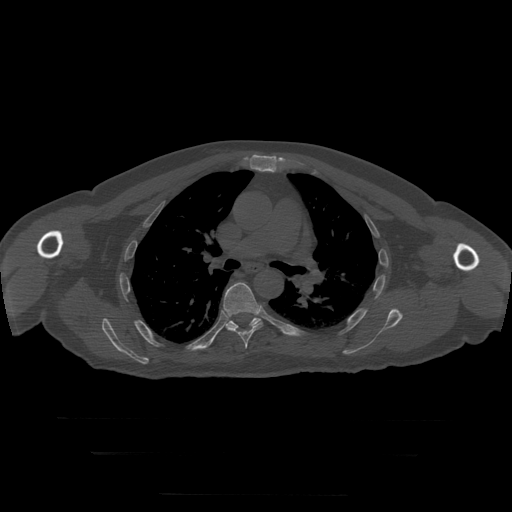
CT including the spine, one axial slice. Position 200 of 397 along the scan axis. Bone window (W 1800 / L 400 HU). 1.25 mm slice thickness. 512 × 512 image matrix, field of view 510 × 510 mm. Patient age 73 years. From the clinical record (not read from this slice): primary cancer: prostate.
Annotated regions visible in this slice (semi-automatically segmented with operator editing):
- T6 vertebra: box from (x=223, y=283) to (x=263, y=349) px
- T7 vertebra: (x=227, y=316)–(x=262, y=328)